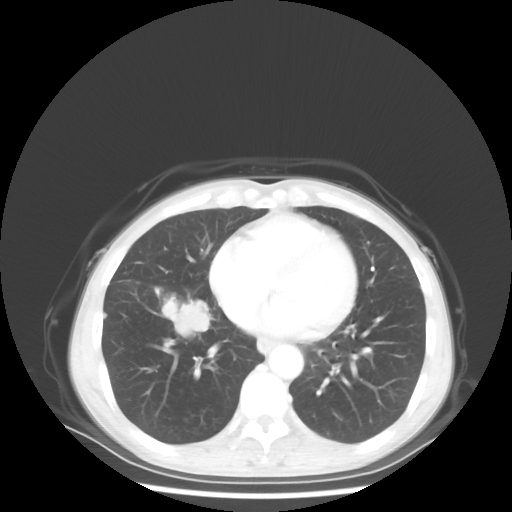
Chest CT, one axial slice. Slice 20 of 56 in the series (ordered by position). Reconstruction kernel STANDARD. 80 kVp. Lung window (W 1500 / L -600 HU). 5 mm slice thickness. 512 × 512 image matrix. Patient: female, 57 years. From the clinical record (not read from this slice): clinical TNM (as recorded): T1c N3 M1a.
Annotated regions visible in this slice (rectangle marked by the reading radiologist):
- lung tumour (recorded histology: adenocarcinoma): bounding box [x1, y1, x2, y2] px = [160, 296, 208, 339]